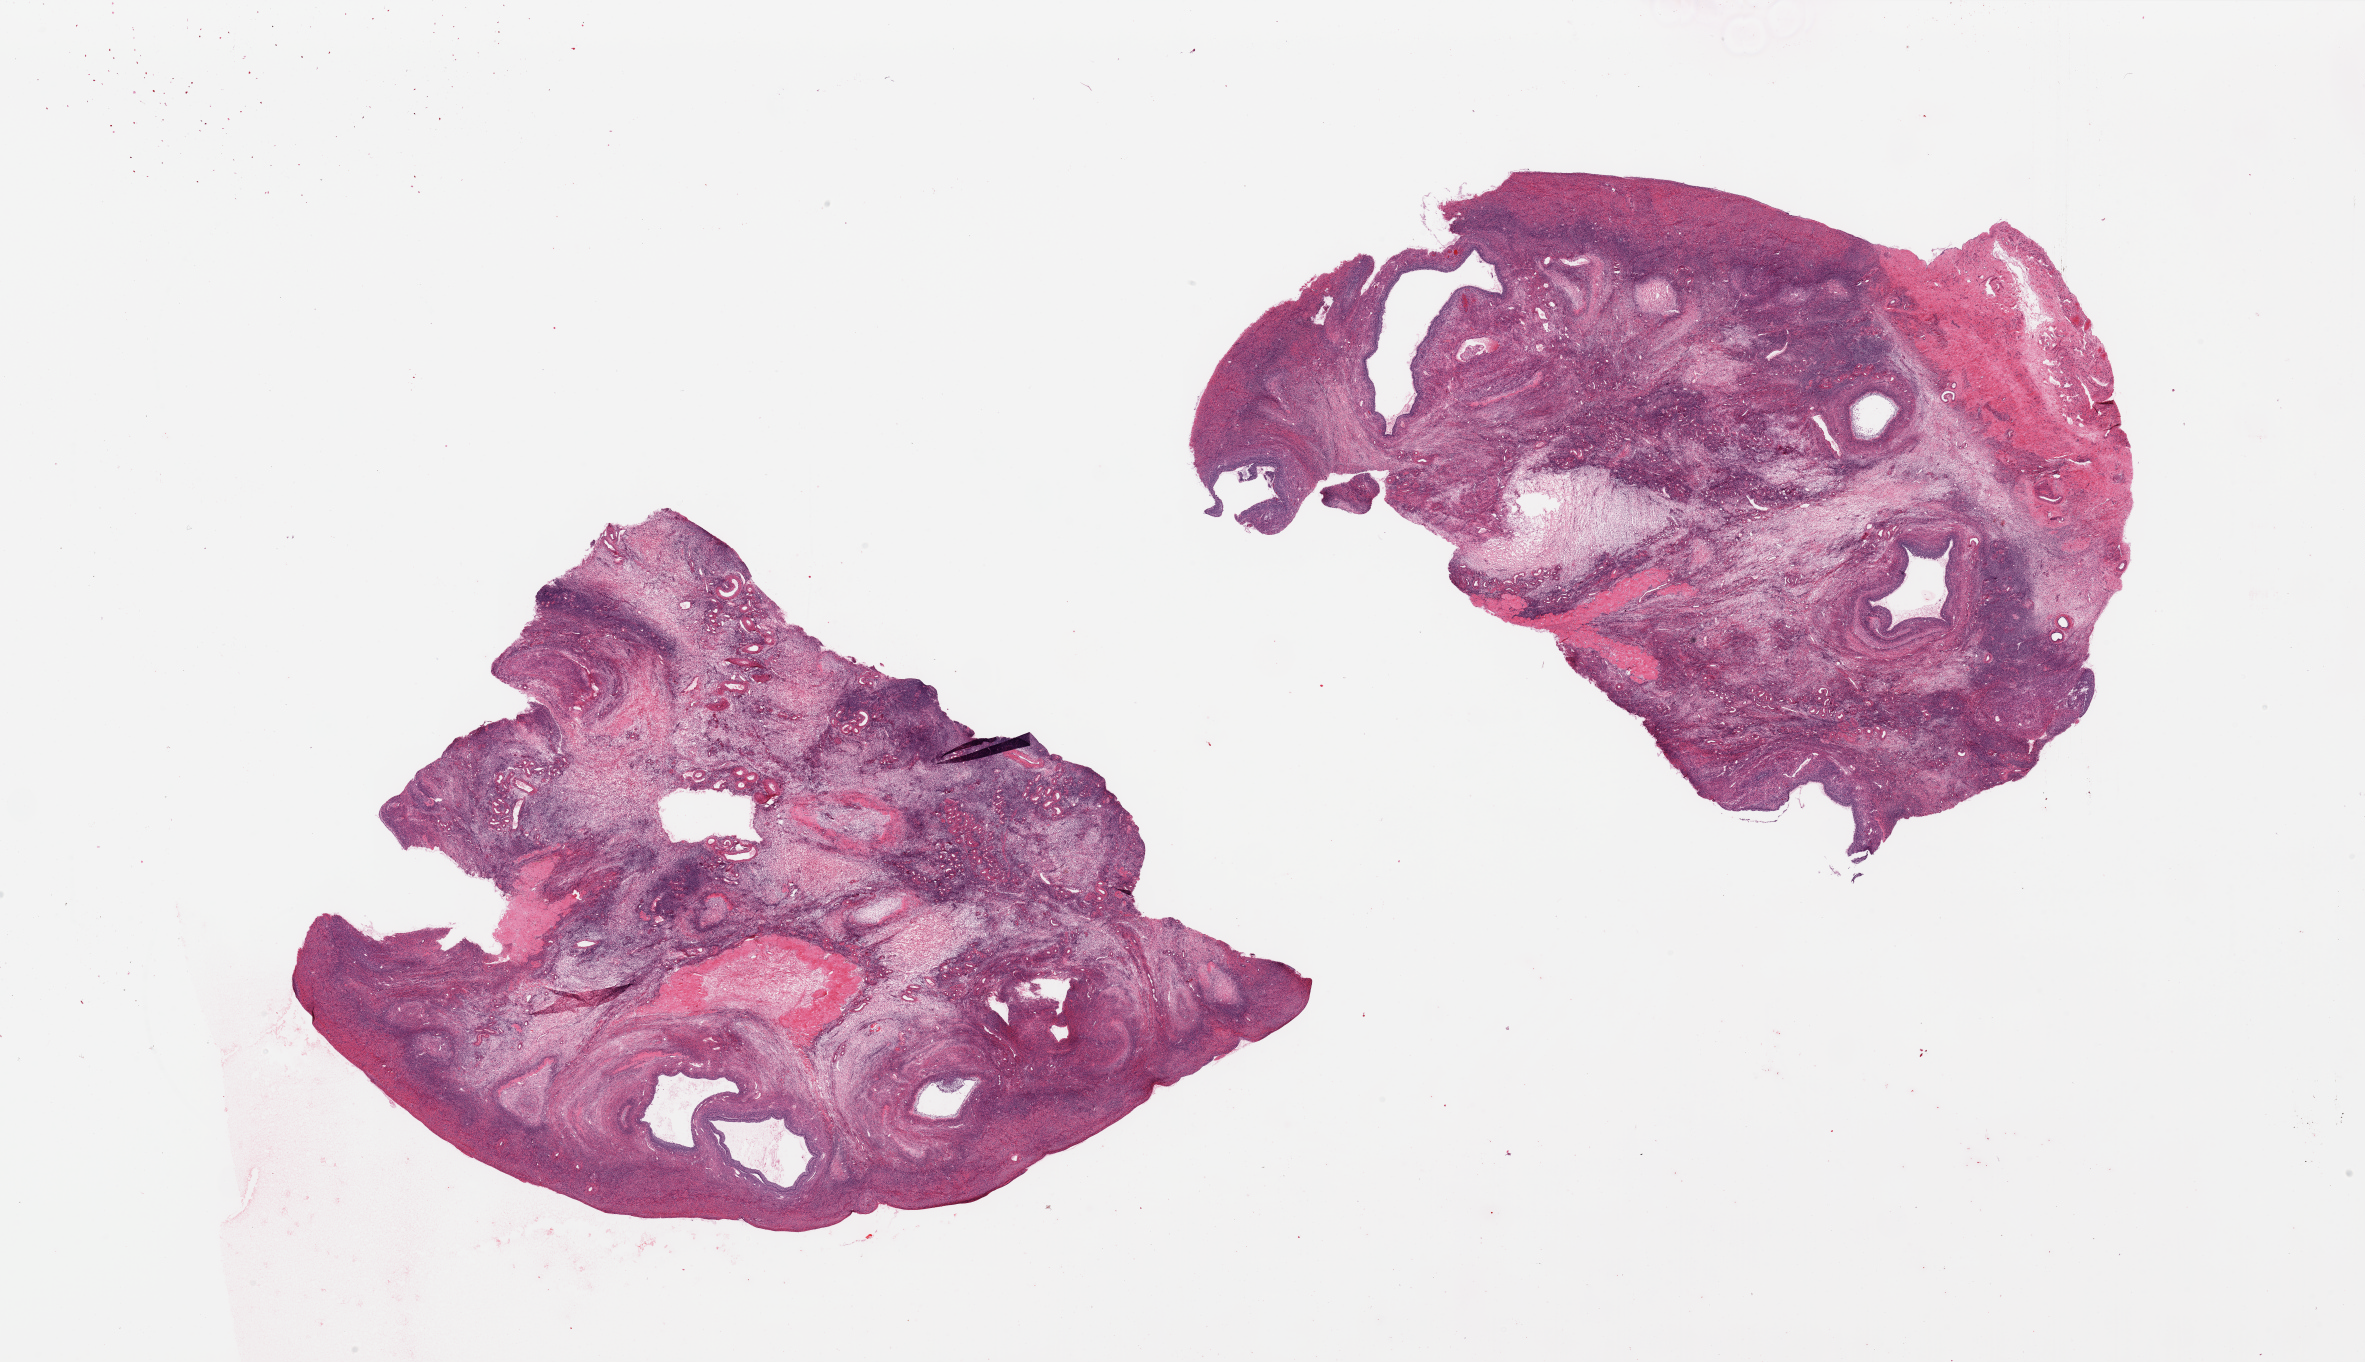
Digitized hematoxylin and eosin (H&E)-stained section — shown as a low-resolution overview of the whole scanned area (about 37.4 x 21.5 mm, from a 20x scan); PAXgene-fixed paraffin-embedded (PFPE) section; section of ovary (target tissue); tissue donor sample. Donor sex: female.
* reviewer comment on this tissue sample: 2 pieces; fertile ovary